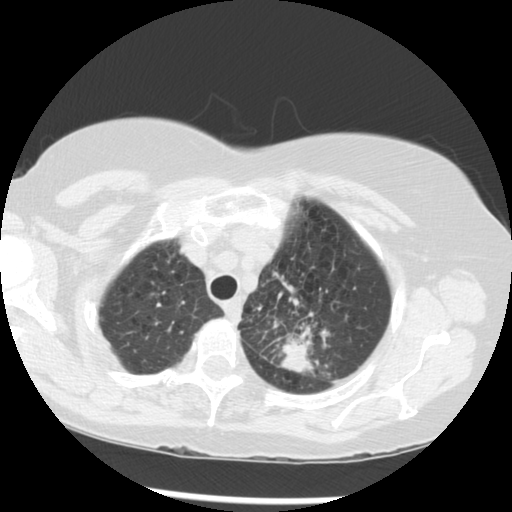
Low-dose screening chest CT, one axial slice; 120 kVp; lung window (W 1500 / L -600 HU); 512 × 512 image matrix, field of view 330 × 330 mm.
Annotated regions visible in this slice (outlined manually by an expert reader):
- lesion 1 (tumor, upper lobe of left lung): bounding box (x1, y1, x2, y2) in pixels: (279, 326, 316, 374)